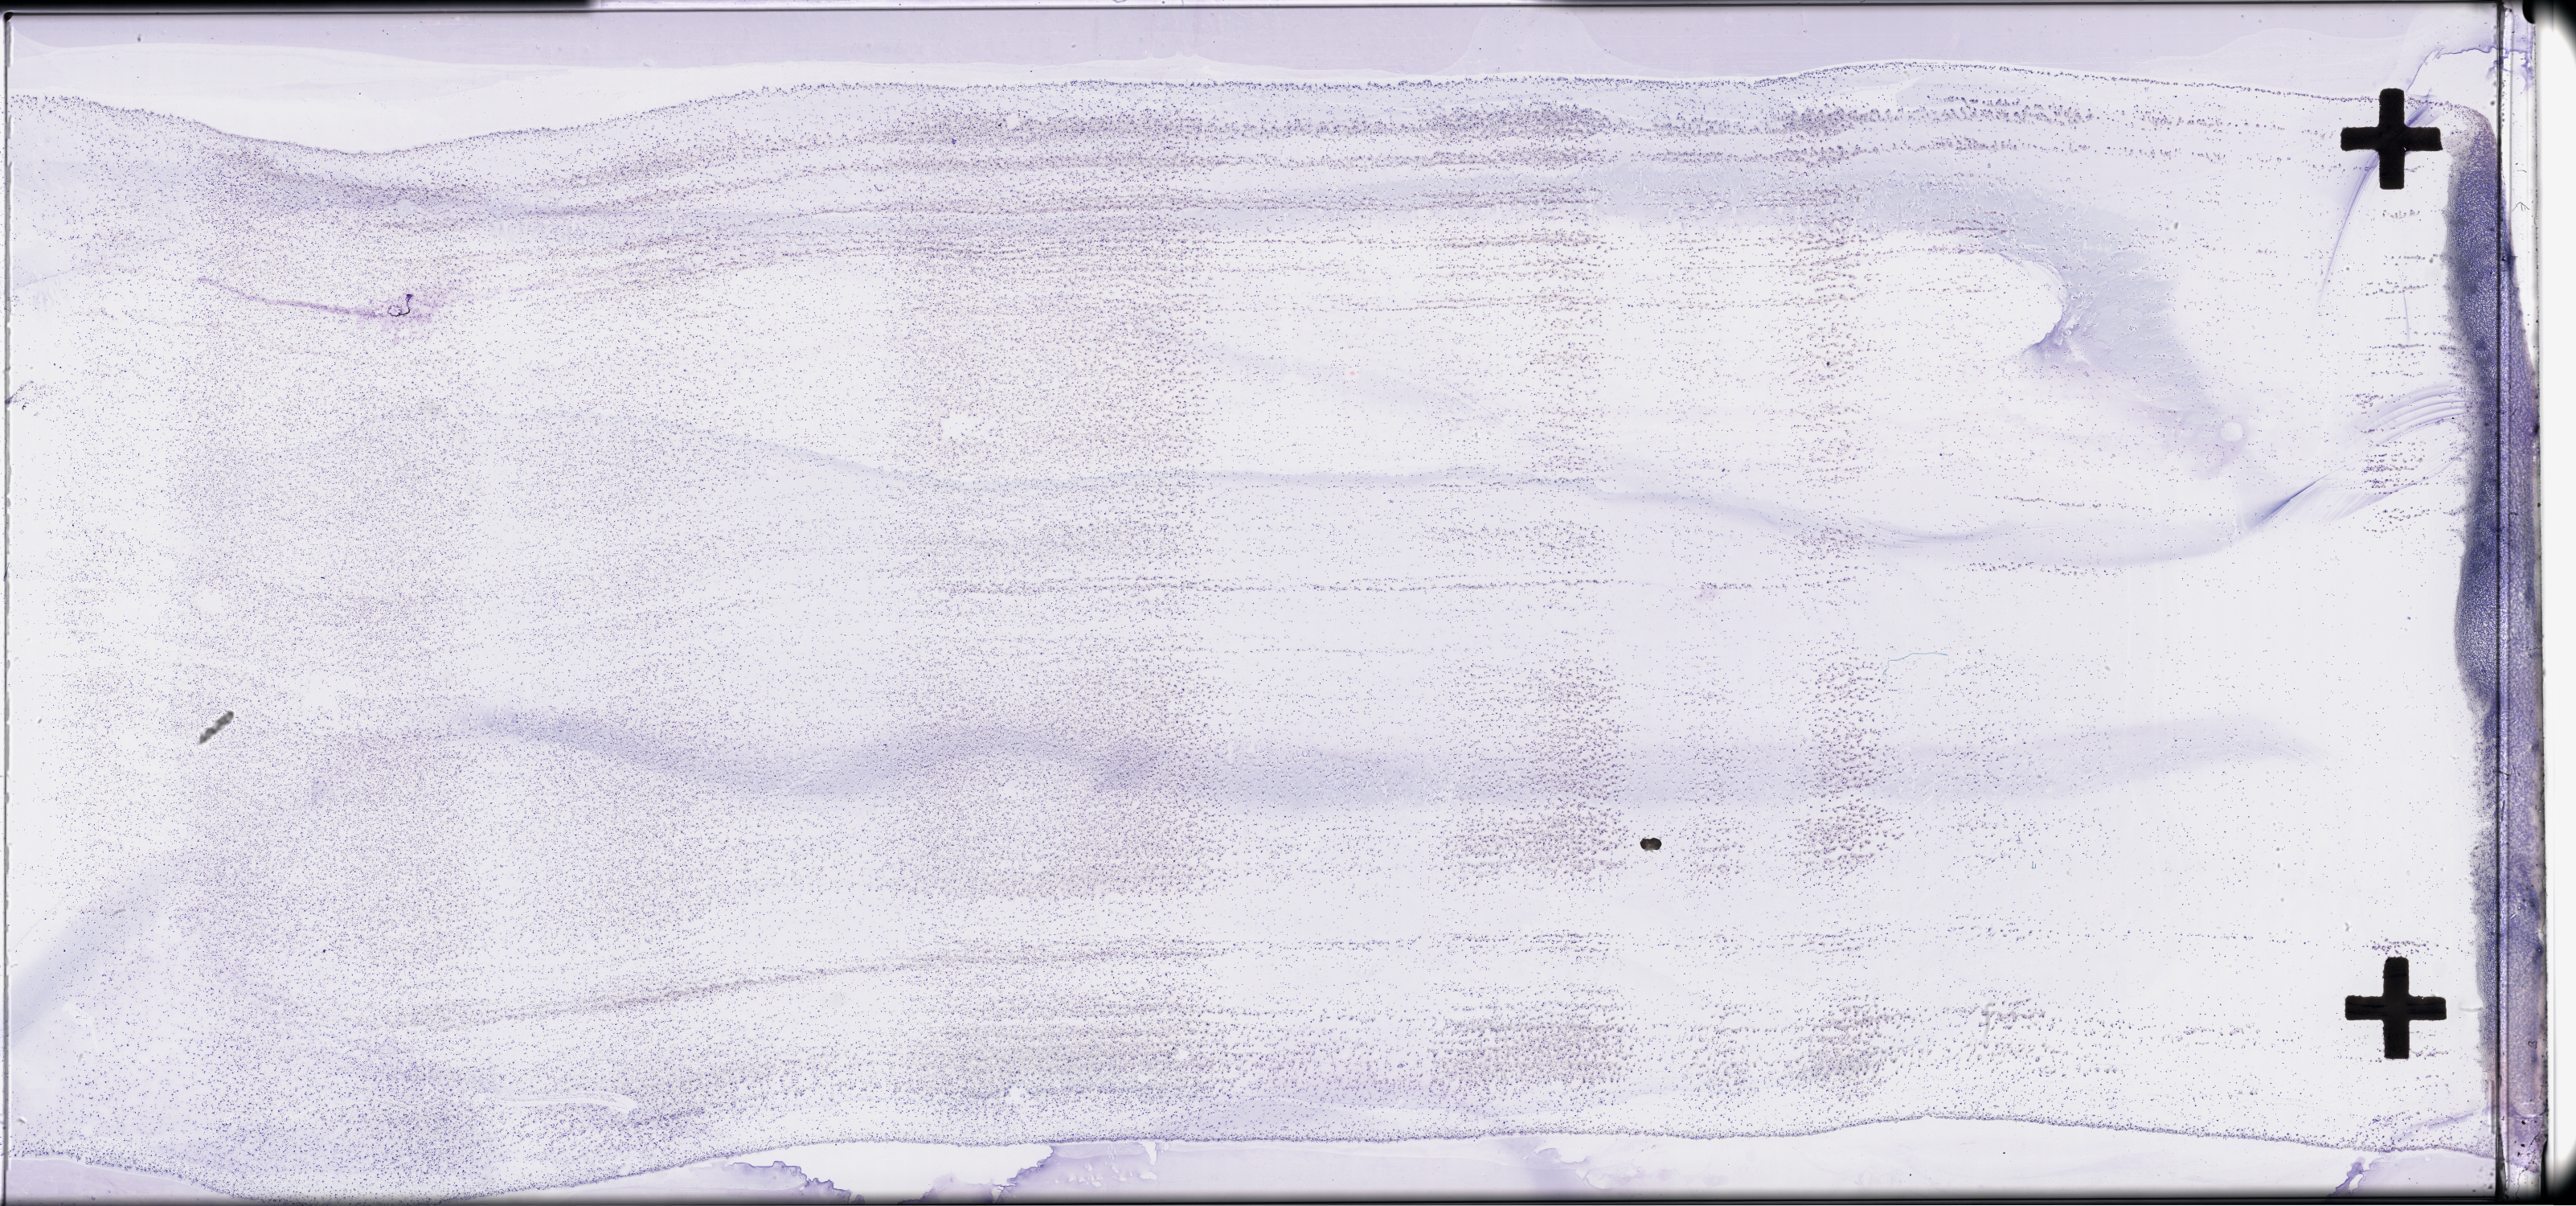
Whole-slide histology image, H&E-stained, low-resolution overview of the scanned area, about 51.8 x 24.2 mm (from a 40x scan); bone marrow (leukaemic) sample. Patient: female, age 70 years. Blasts: 90%.
- FAB classification: M1
- diagnosis: Acute Myeloid Leukemia